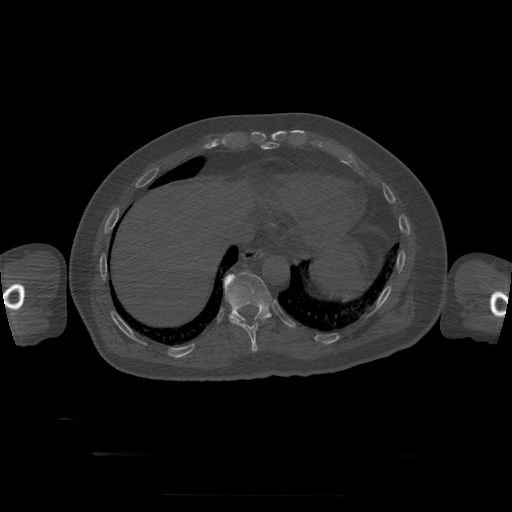
CT including the spine, one axial slice. Position 112 of 397 along the scan axis. Bone window (W 1800 / L 400 HU). 1.25 mm slice thickness. 512 × 512 image matrix, field of view 510 × 510 mm. Patient age 73 years. Case-level facts recorded for this patient, not image findings: primary cancer: prostate.
Structures marked on this image (semi-automatically segmented with operator editing):
- T10 vertebra: box from (x=229, y=317) to (x=270, y=352) px
- T11 vertebra: (x=224, y=272)–(x=272, y=323)